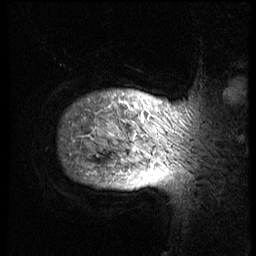
Breast MRI (dynamic contrast-enhanced), one sagittal slice; position 67 of 74 along the scan axis; 3 images stored at this slice position (order not interpretable as contrast timing); 1.5 T; TE 4.2 ms, TR 8.9 ms; 256 × 256 image matrix, field of view 200 × 200 mm. Patient: female, 57 years. Case-level facts recorded for this patient, not image findings: setting: breast cancer imaged before/during neoadjuvant chemotherapy; receptor status: HER2-positive.
Annotated regions visible in this slice (semi-automatic segmentation, software-assisted and operator-edited):
- analysis volume of interest (the breast-tissue region the enhancement analysis was run in; not a lesion): bounding box <48,65,237,175> (left, top, right, bottom; pixels)
- tumour enhancement mask (voxels above the 140 % enhancement threshold inside the analysis volume of interest): <72,101,190,175>